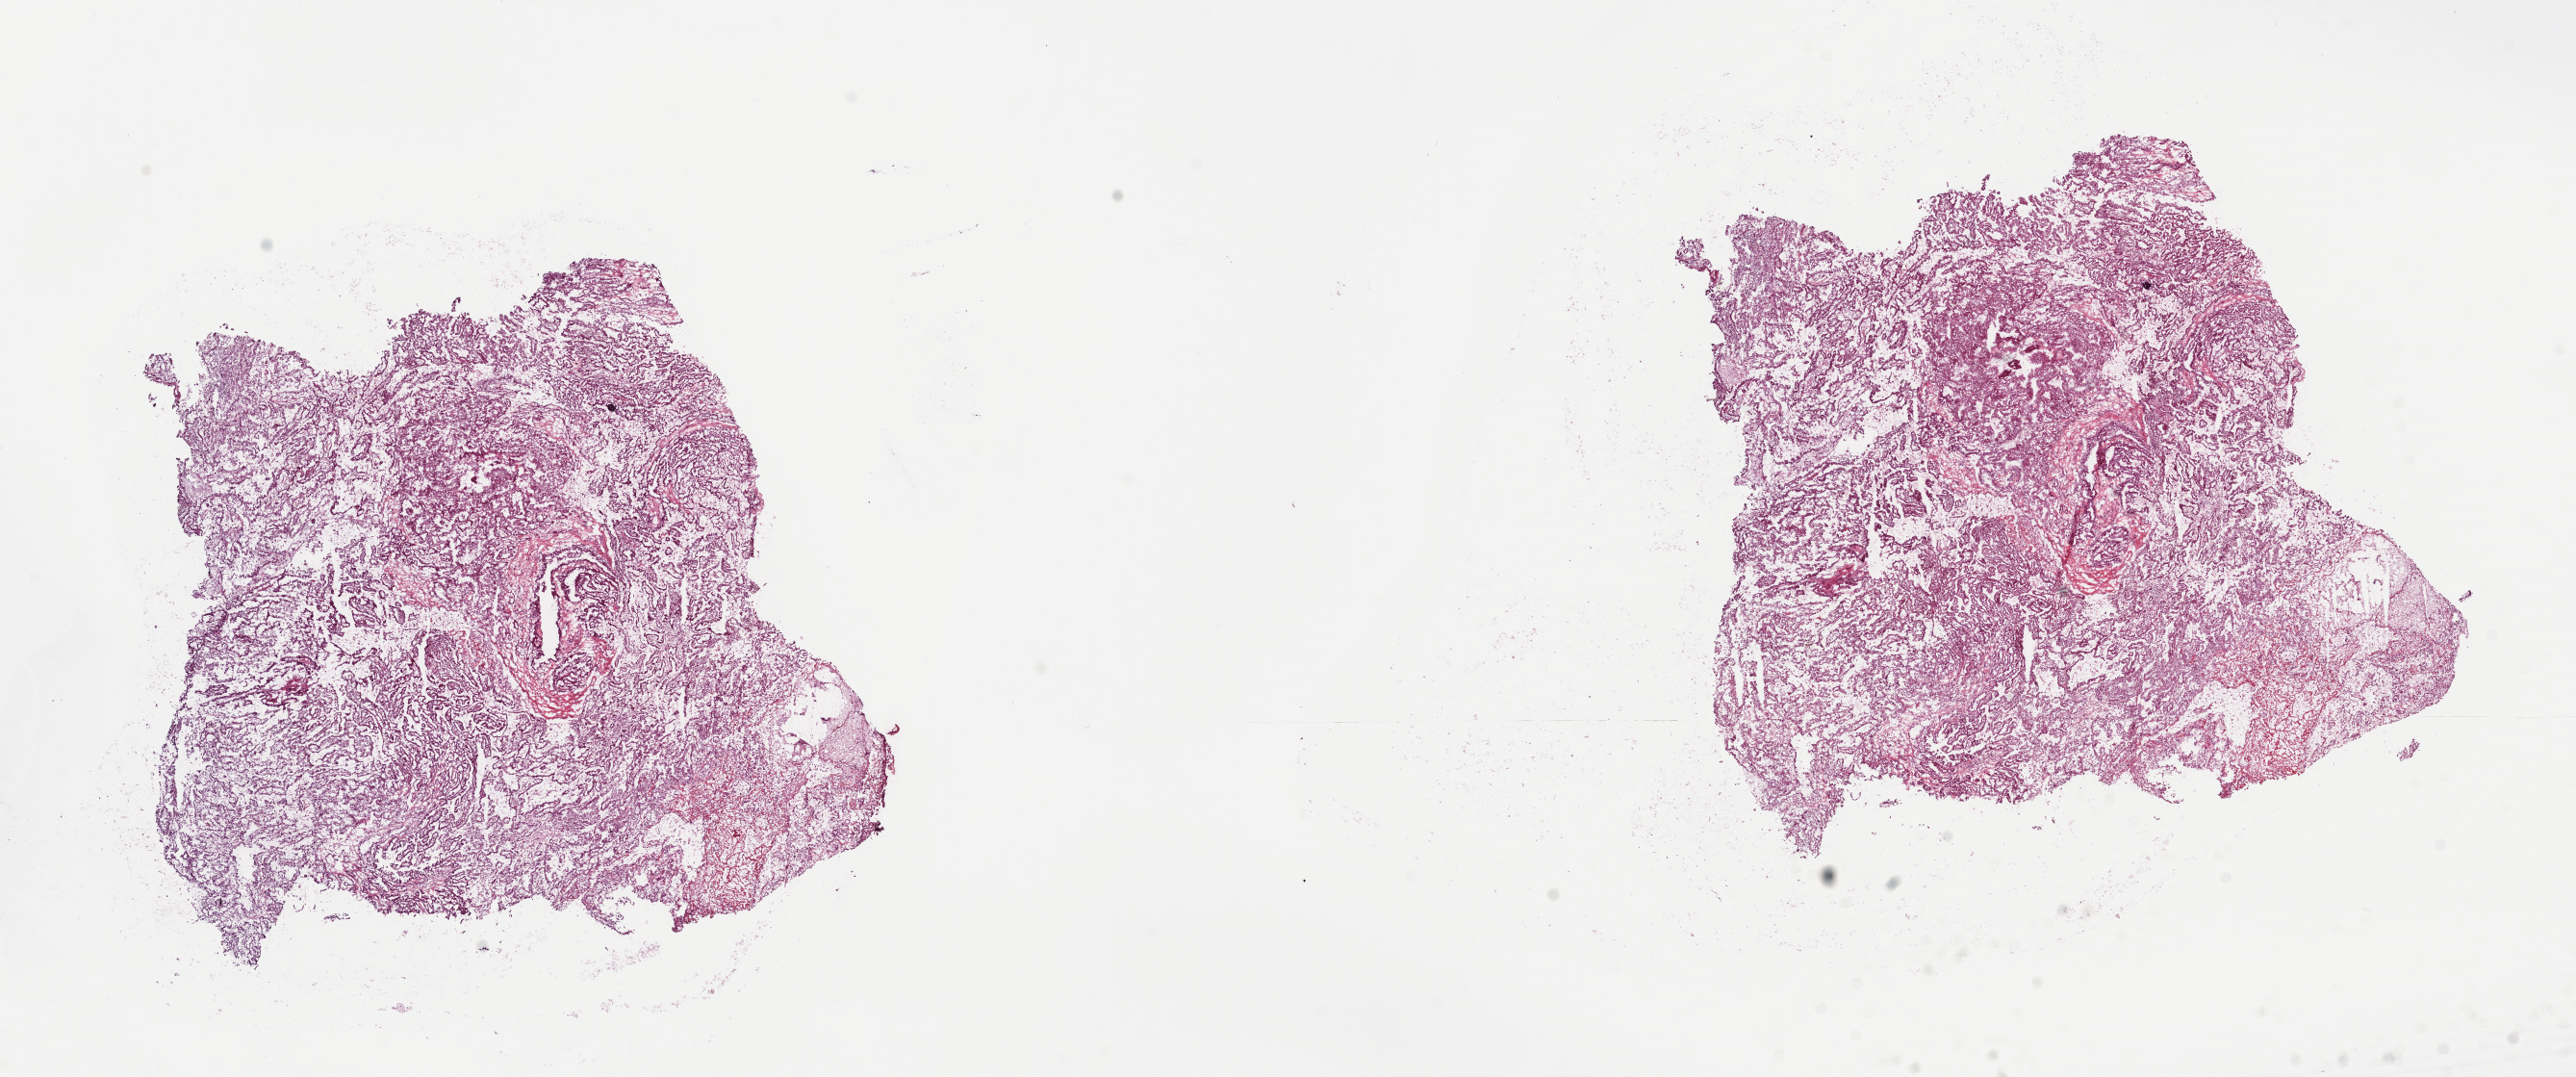
Whole-slide histology image, H&E-stained, low-resolution overview of the scanned area, about 21.1 x 8.8 mm (slide scanned at 40x), frozen section from the top of the tissue portion, primary tumour sample from the kidney. Patient: male, age at initial diagnosis 43 years. Pathologist review of this section (percent, as recorded): tumour cells 85%, tumour nuclei 85%.
Histologic diagnosis: Papillary adenocarcinoma, NOS.